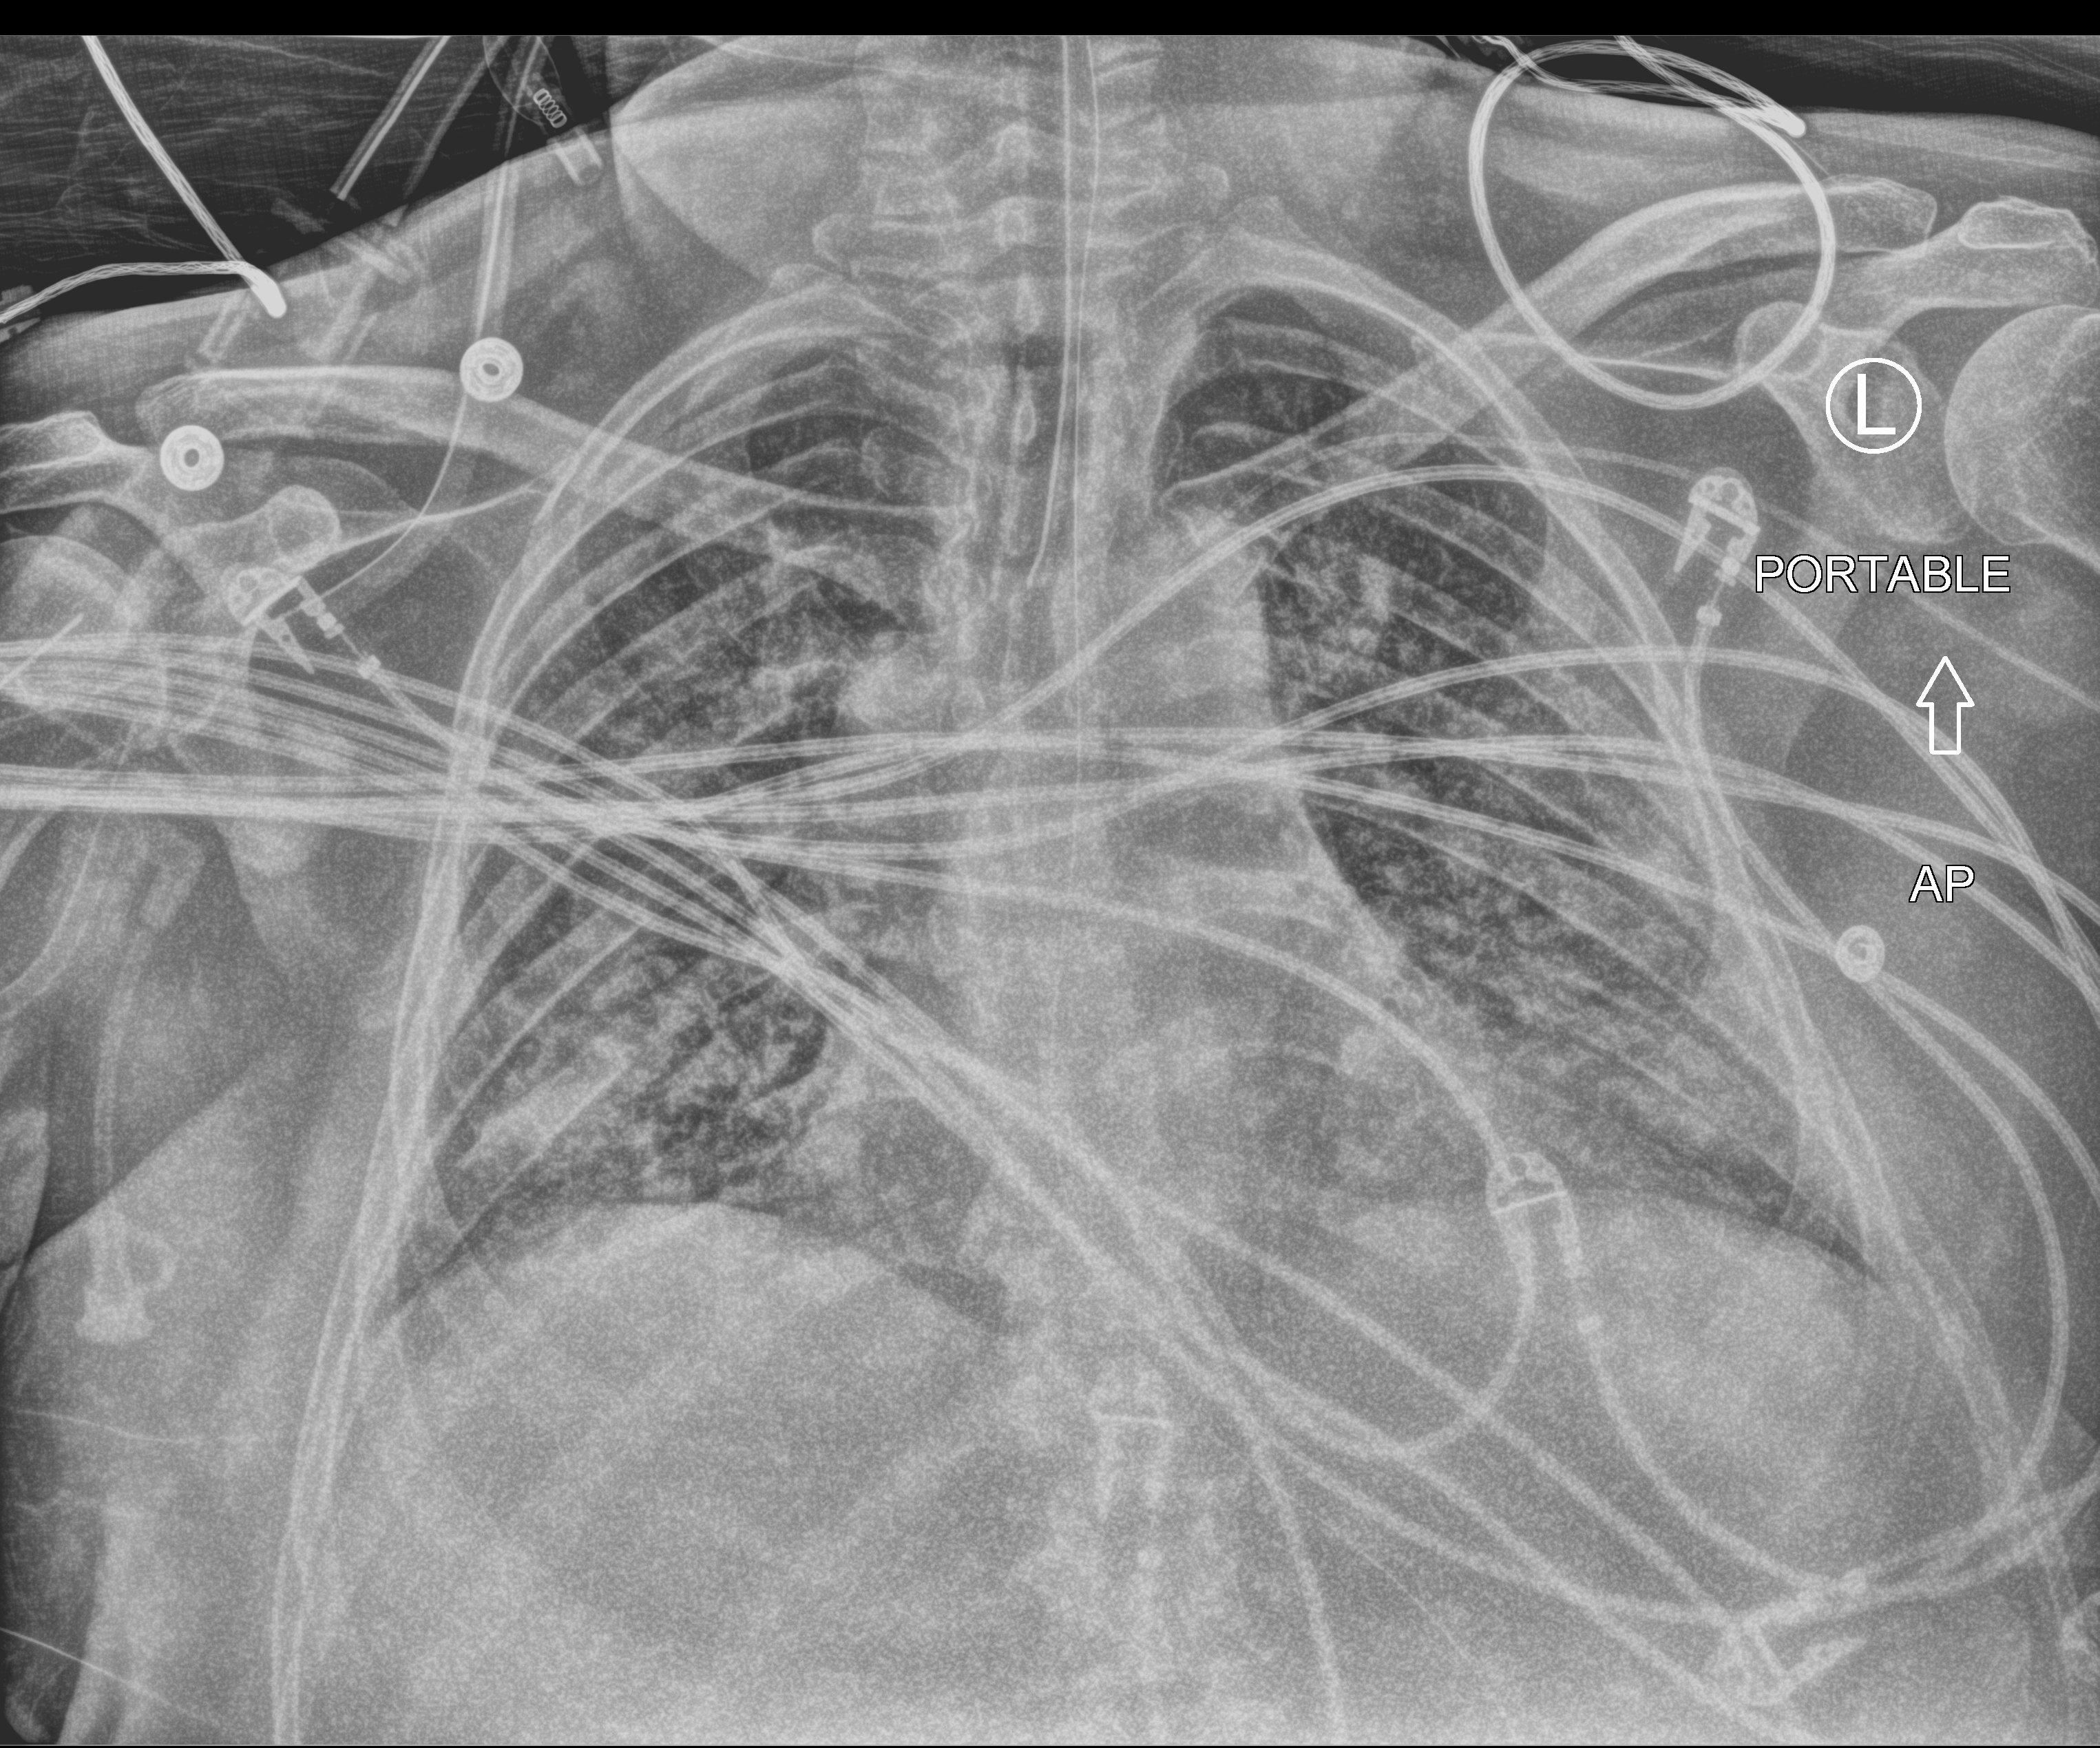
Portable chest radiograph; anteroposterior (AP) projection. Patient hospitalised with COVID-19; male, aged 18–59 years.
From the hospital-stay record, not from the radiograph (when in the stay this image was taken is not recorded): diabetes (admission record): no; admitted to intensive care during this hospital stay: yes.